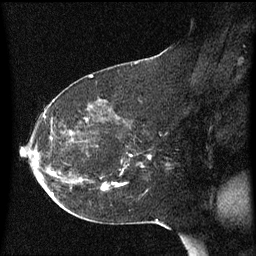
Breast MRI (dynamic contrast-enhanced), one sagittal slice. Slice 33 of 60 in the series (ordered by position). Dynamic contrast-enhanced series, image 2 of 3 at this slice position (ordered by acquisition). 1.5 T. TE 4.2 ms, TR 8.4 ms. 2 mm slice thickness. 256 × 256 image matrix, field of view 200 × 200 mm. Patient: female, 54 years. Case-level facts recorded for this patient, not image findings: setting: breast cancer imaged before/during neoadjuvant chemotherapy; receptor status: HR-positive, HER2-negative.
Annotated regions visible in this slice (semi-automatically segmented with operator editing):
- analysis volume of interest (the breast-tissue region the enhancement analysis was run in; not a lesion): box from (x=98, y=120) to (x=169, y=191) px
- tumour enhancement mask (voxels above the 70 % enhancement threshold inside the analysis volume of interest): (x=103, y=186)–(x=109, y=191)